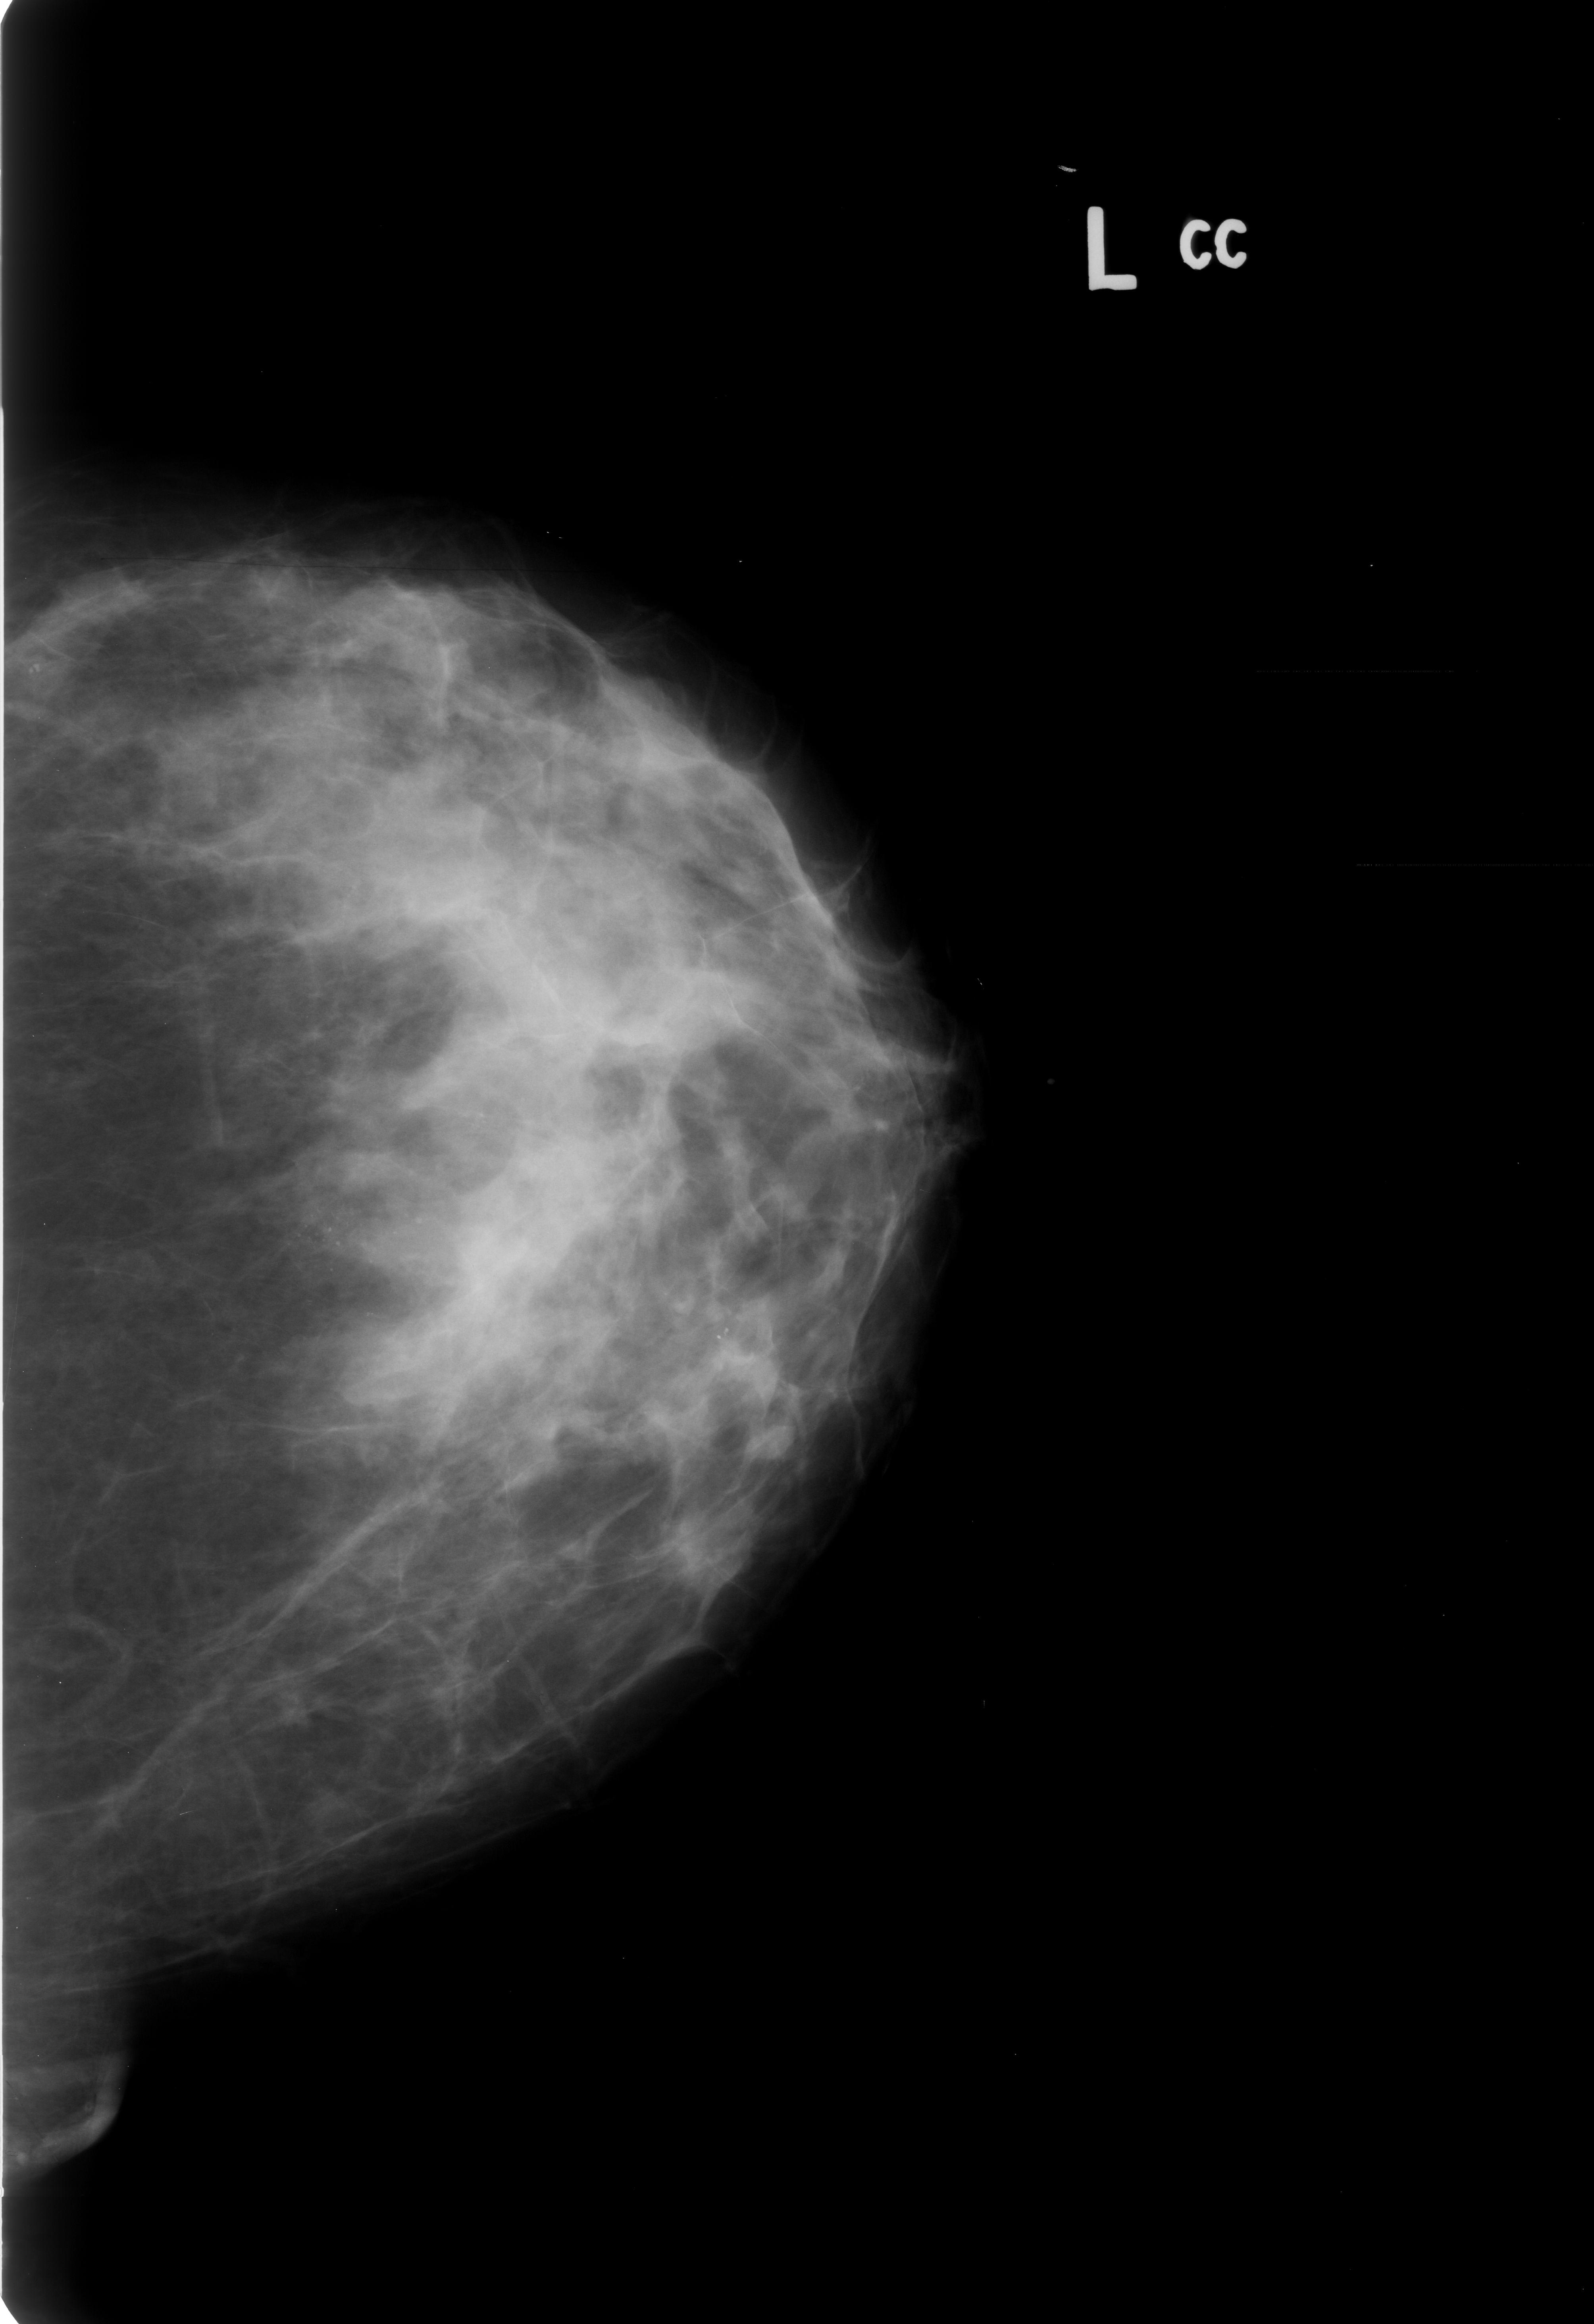
Mammogram (digitized film); left breast; craniocaudal (CC) view; 1594 × 2324 image matrix.
Marked abnormalities (boxes around the expert regions of interest):
- Finding 1 of 2: calcifications, morphology pleomorphic, distribution segmental; BI-RADS assessment category 4; subtlety rating 3 on a 1 (subtle) to 5 (obvious) scale; pathology (as recorded): benign: bounding box (x1, y1, x2, y2) in pixels: (288, 1184, 464, 1299)
- Finding 2 of 2: calcifications, morphology pleomorphic, distribution segmental; BI-RADS assessment category 4; pathology (as recorded): benign: (438, 1057, 525, 1144)